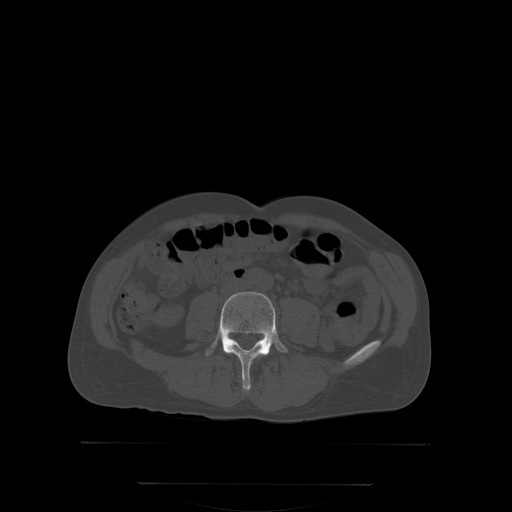
CT including the spine, one axial slice; slice 108 of 350 in the series (ordered by position); bone window (W 1800 / L 400 HU); 2.5 mm slice thickness; 512 × 512 image matrix, field of view 500 × 500 mm. Male patient, age 58 years. Case-level facts recorded for this patient, not image findings: primary cancer: prostate.
Outlined on this slice (semi-automatically segmented with operator editing):
- L4 vertebra: bounding box (x1, y1, x2, y2) in pixels: (205, 292, 288, 391)